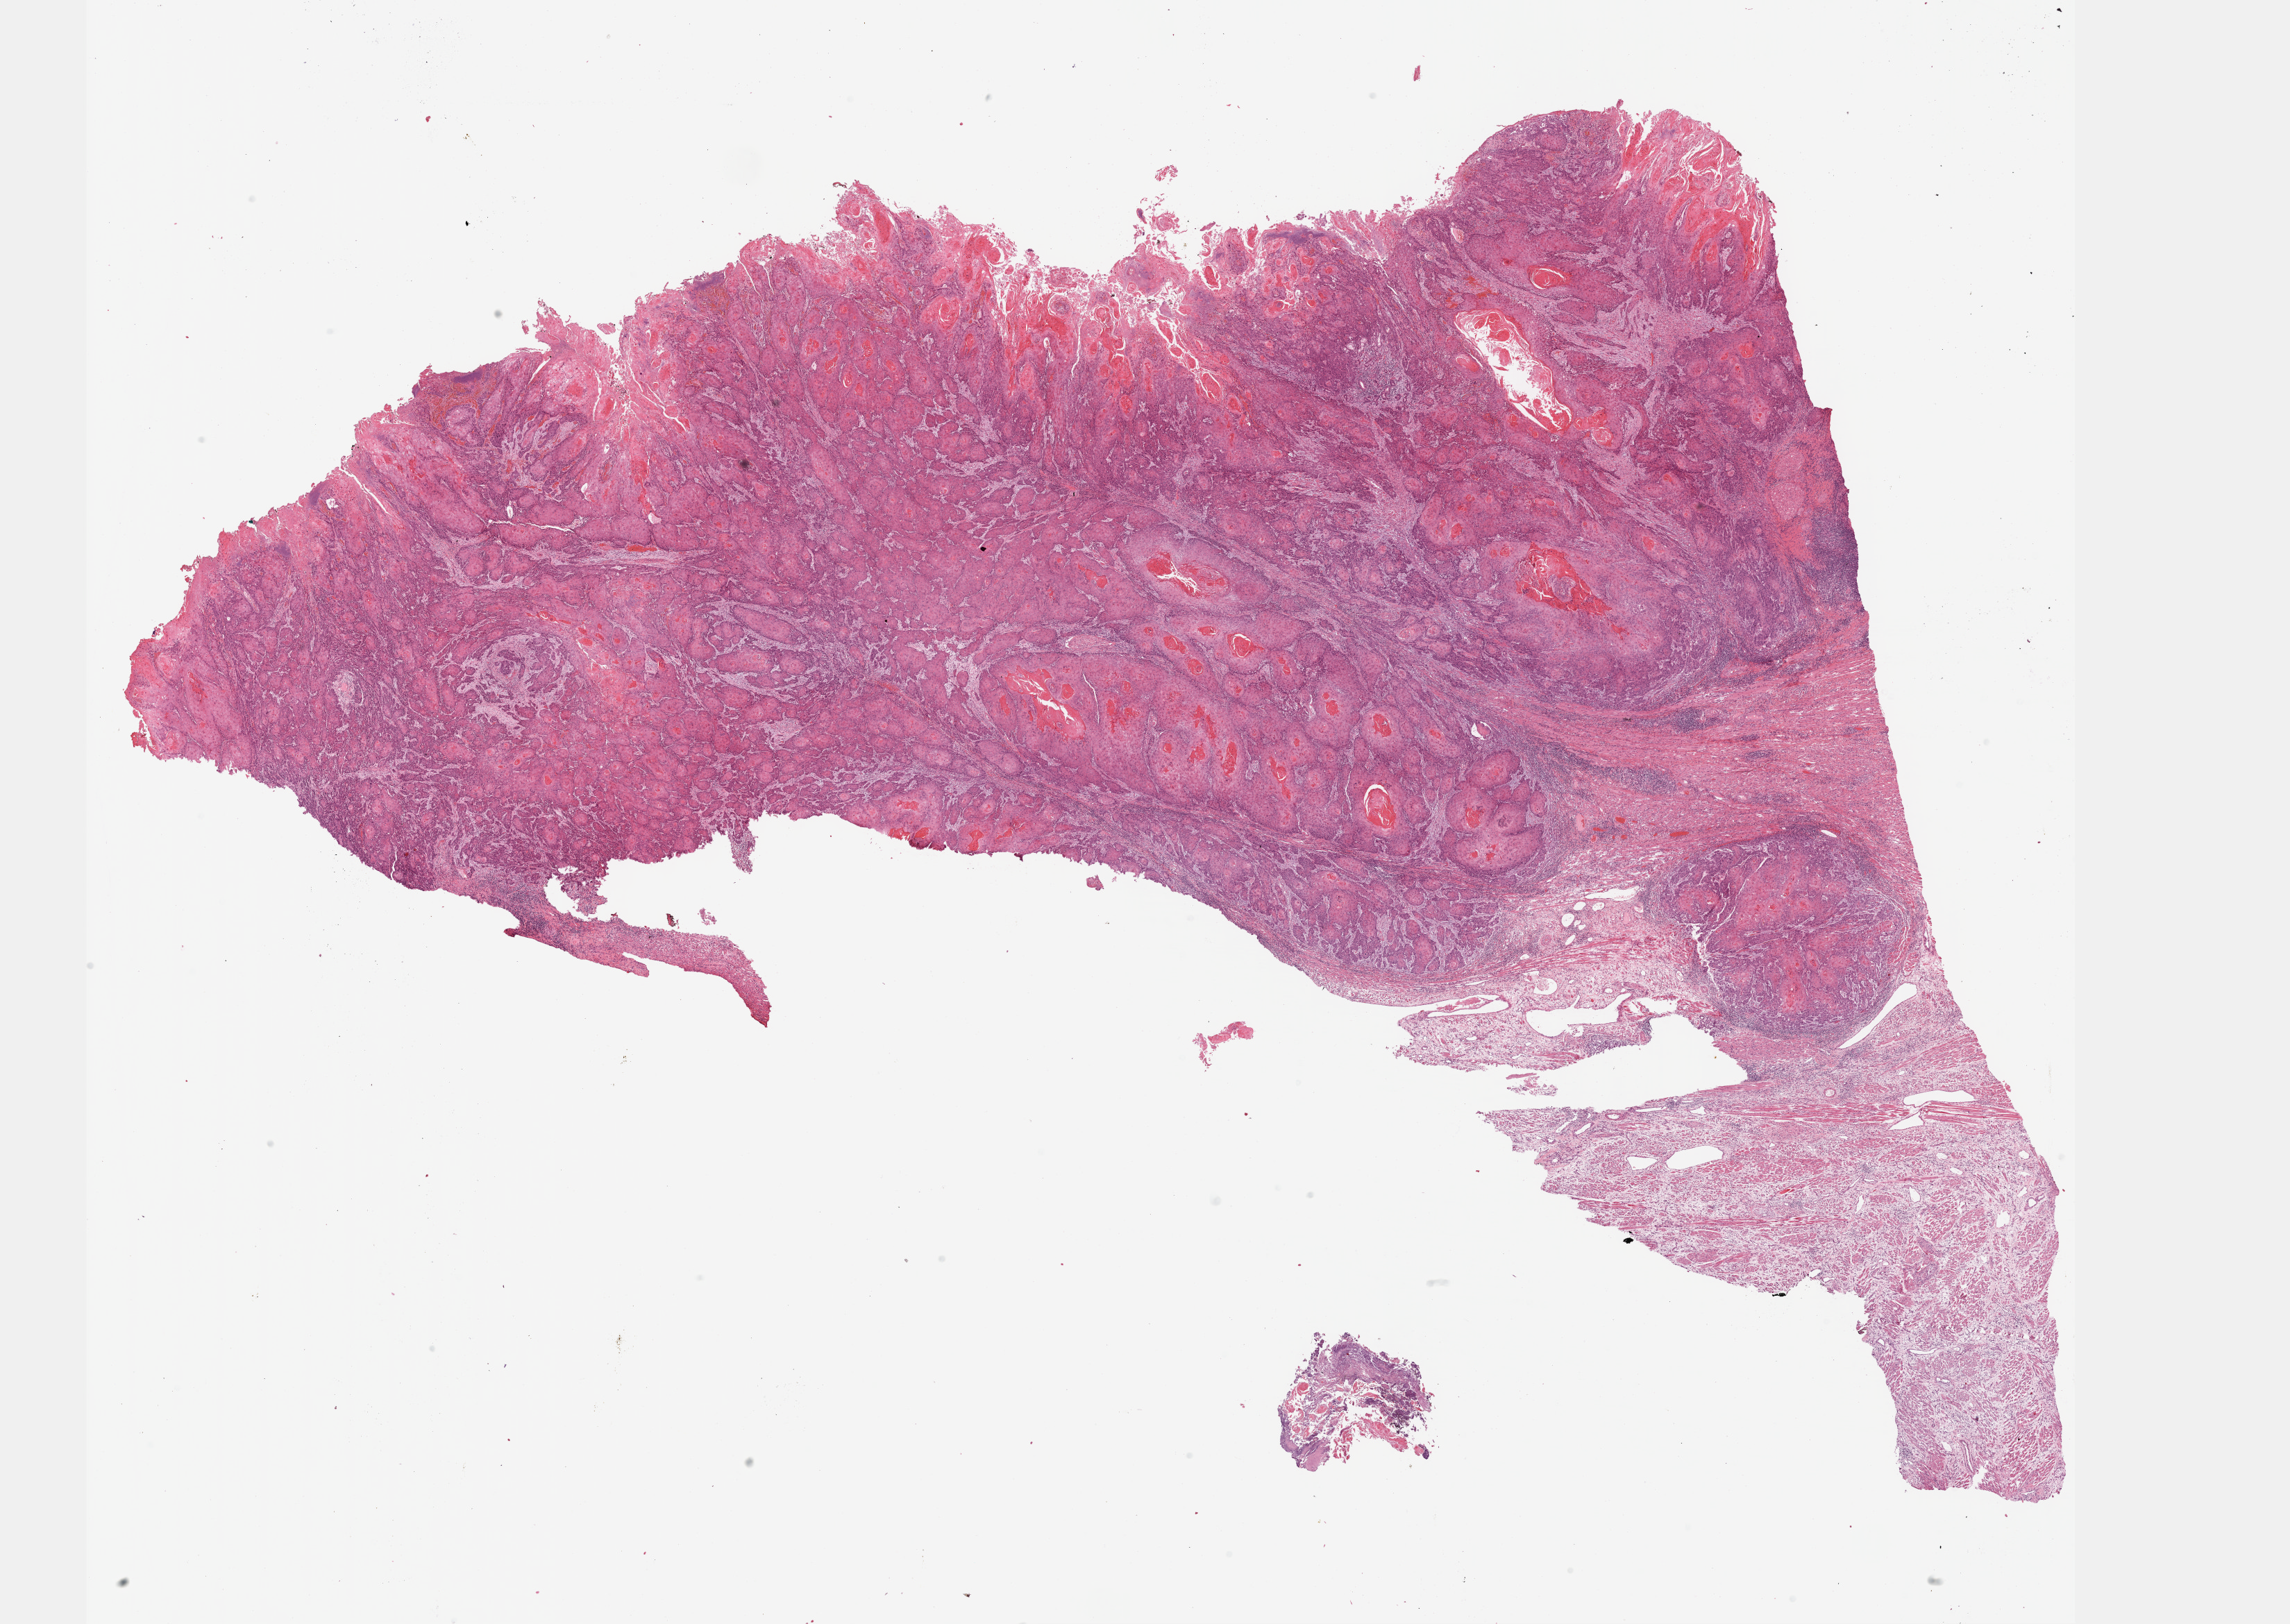
Digitized H&E-stained tissue section (whole slide) — low-resolution overview of the scanned area, about 26.7 x 18.9 mm. FFPE section. Head and neck, primary tumour sample. Male, age 42 years at initial diagnosis. Histologic grade: G1 (well differentiated).
TNM: T3 N2b M0. Pathologic diagnosis: Squamous cell carcinoma, NOS (floor of mouth, NOS). AJCC pathologic stage: IVA (7th edition).